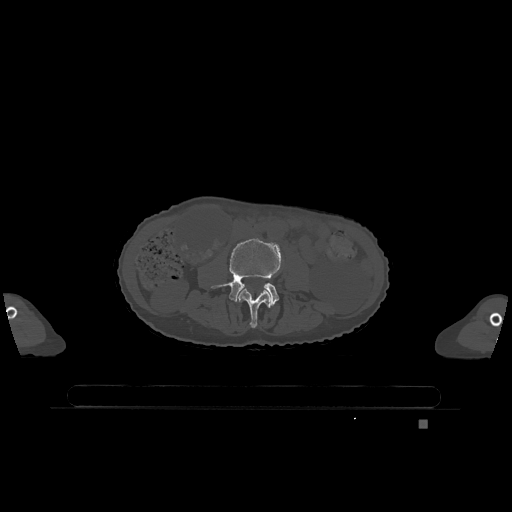
CT including the spine, one axial slice; position 324 of 1317 along the scan axis; bone window (W 1800 / L 400 HU); 0.5 mm slice thickness; 512 × 512 image matrix, field of view 500 × 500 mm. Patient: female, 74 years. From the clinical record (not read from this slice): primary cancer: lung.
Outlined on this slice (semi-automatically segmented with operator editing):
- L3 vertebra: bounding box (x1, y1, x2, y2) in pixels: (238, 288, 271, 328)
- L4 vertebra: (211, 238, 281, 306)